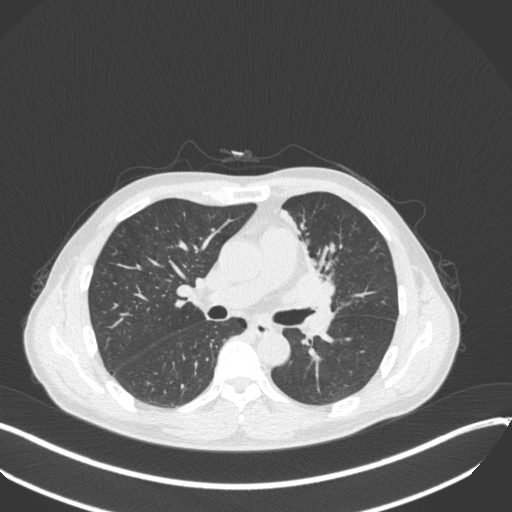
Chest CT, one axial slice; position 191 of 411 along the scan axis; reconstruction kernel B31f; 120 kVp; lung window (W 1500 / L -600 HU); 1 mm slice thickness; 512 × 512 image matrix. Patient: male, 56 years. From the clinical record (not read from this slice): clinical TNM (as recorded): T2a N0 M0.
Outlined on this slice (bounding box drawn by a radiologist):
- lung tumour (recorded histology: squamous cell carcinoma): box from (x=282, y=254) to (x=343, y=314) px